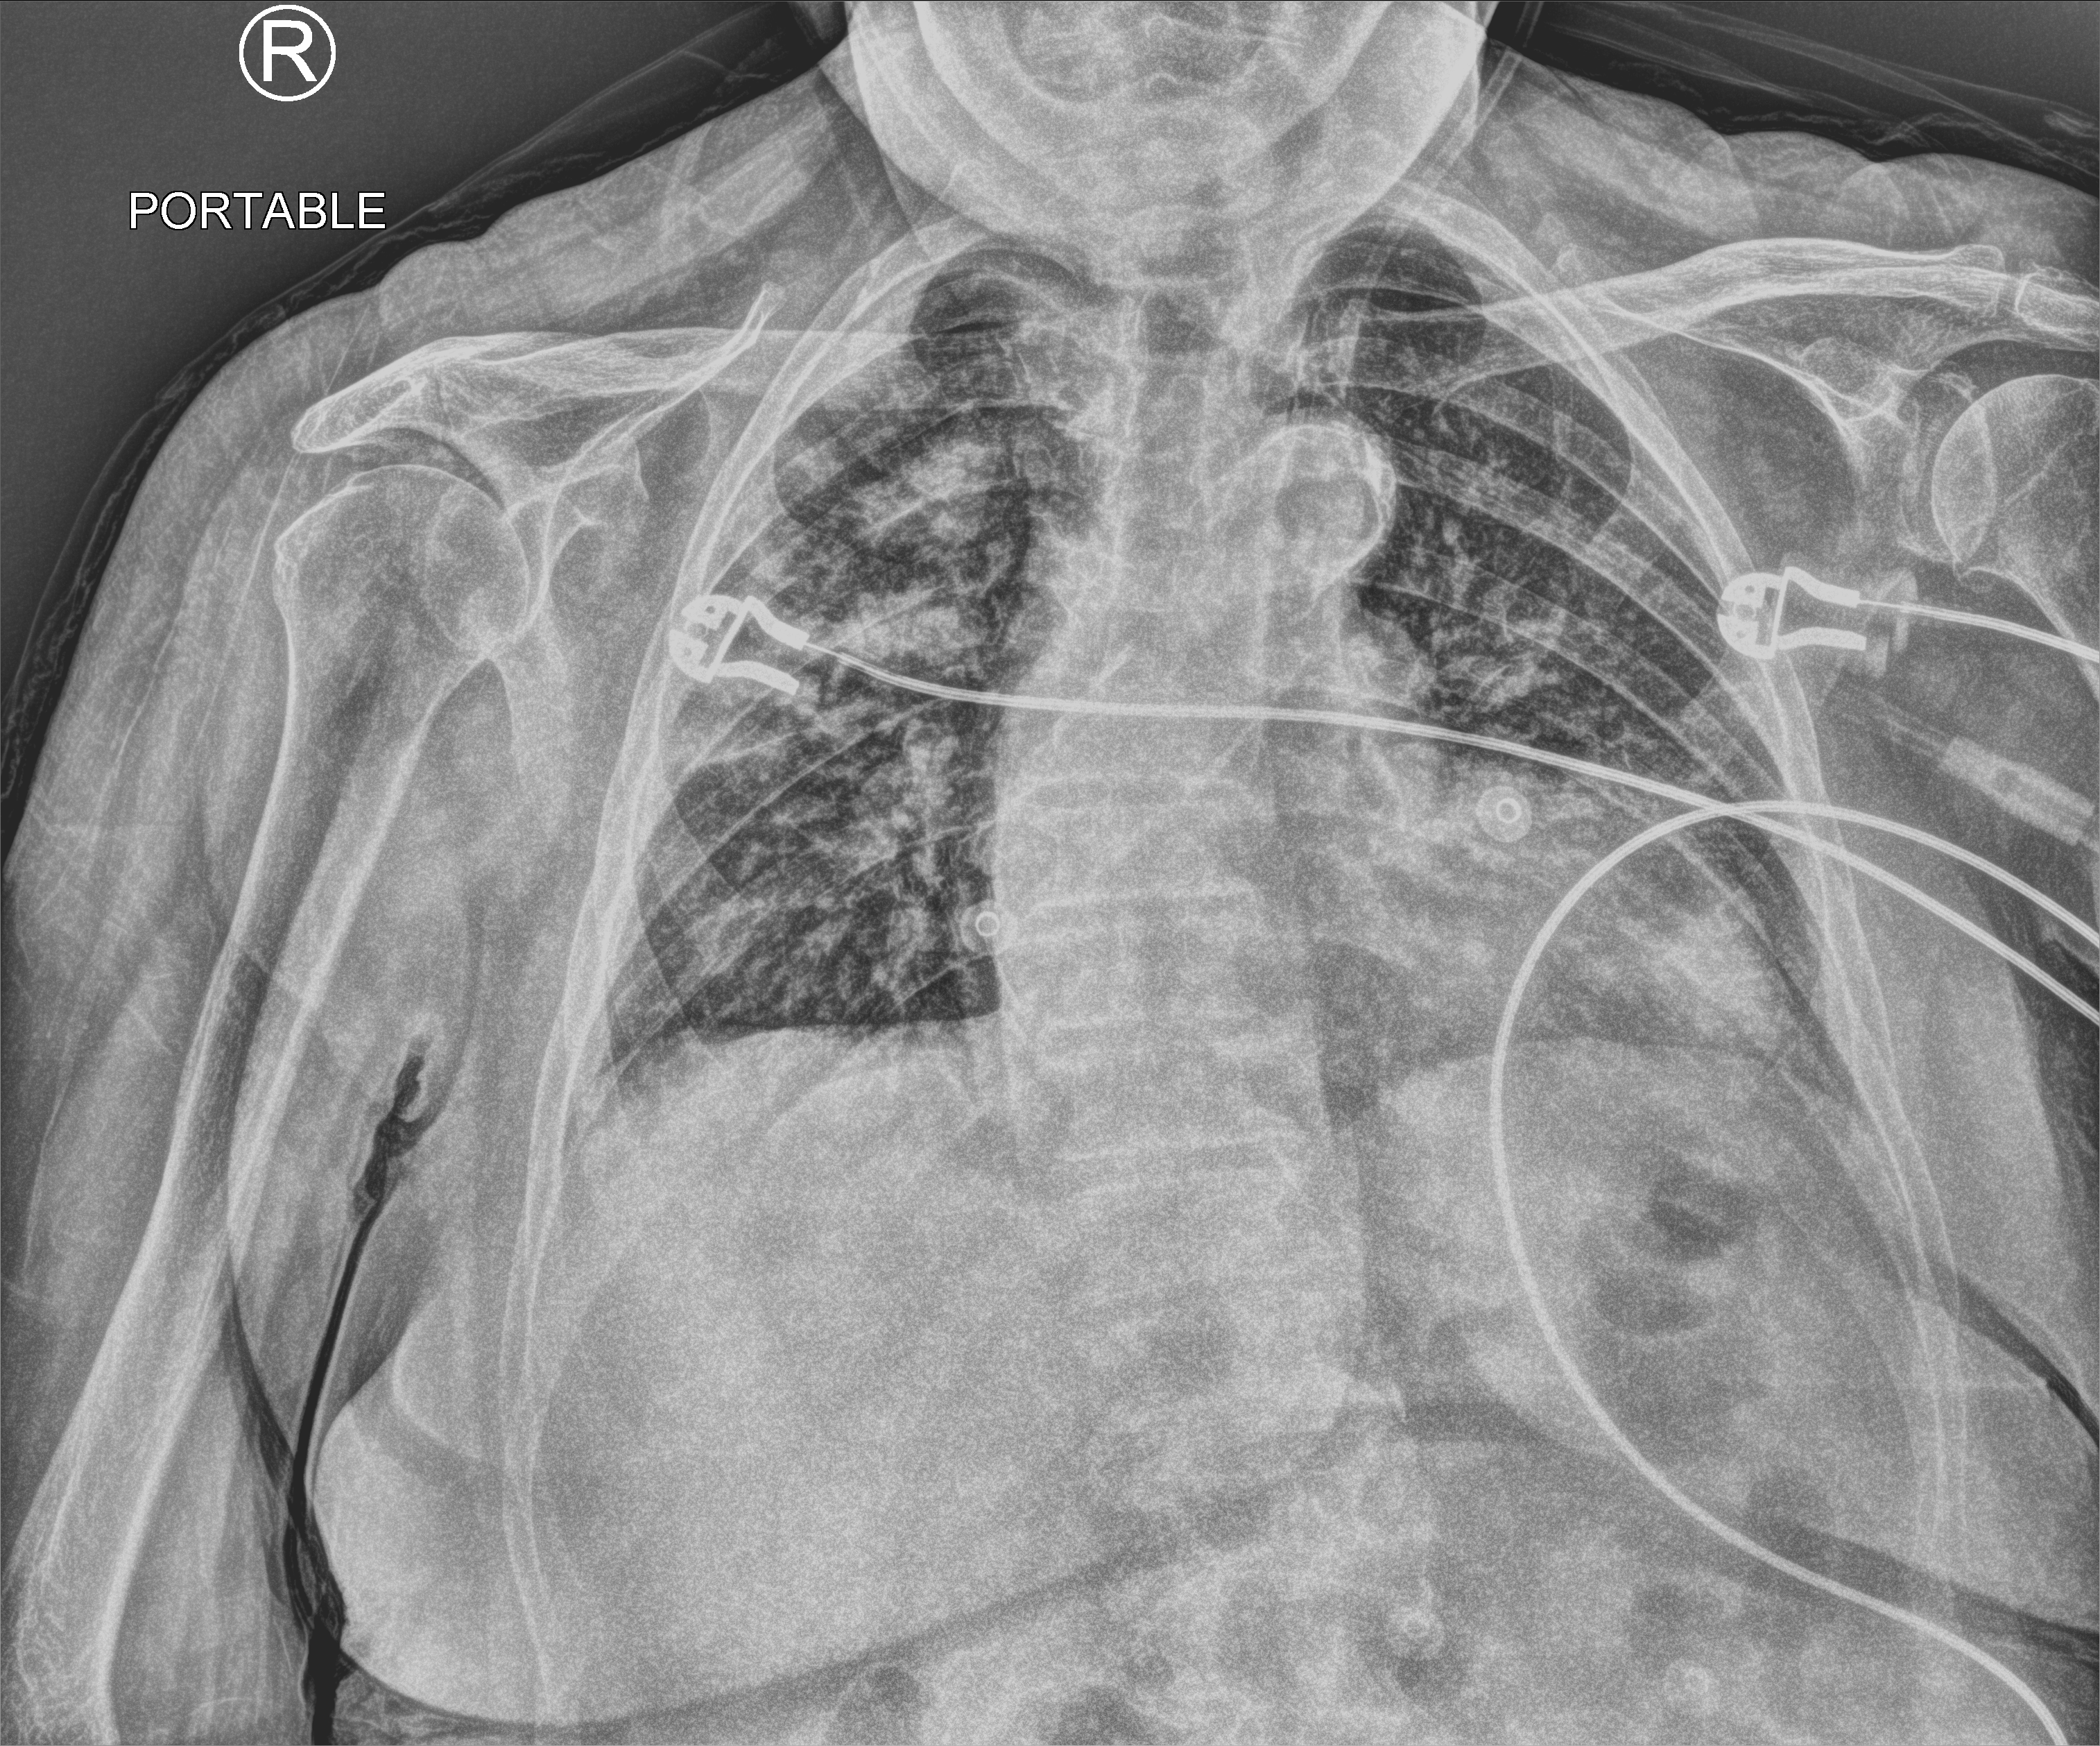
Bedside chest radiograph (computed radiography); anteroposterior (AP) projection. Female patient hospitalised with COVID-19, age 75–90 years.
From the hospital-stay record, not from the radiograph (when in the stay this image was taken is not recorded):
- diabetes (admission record): no